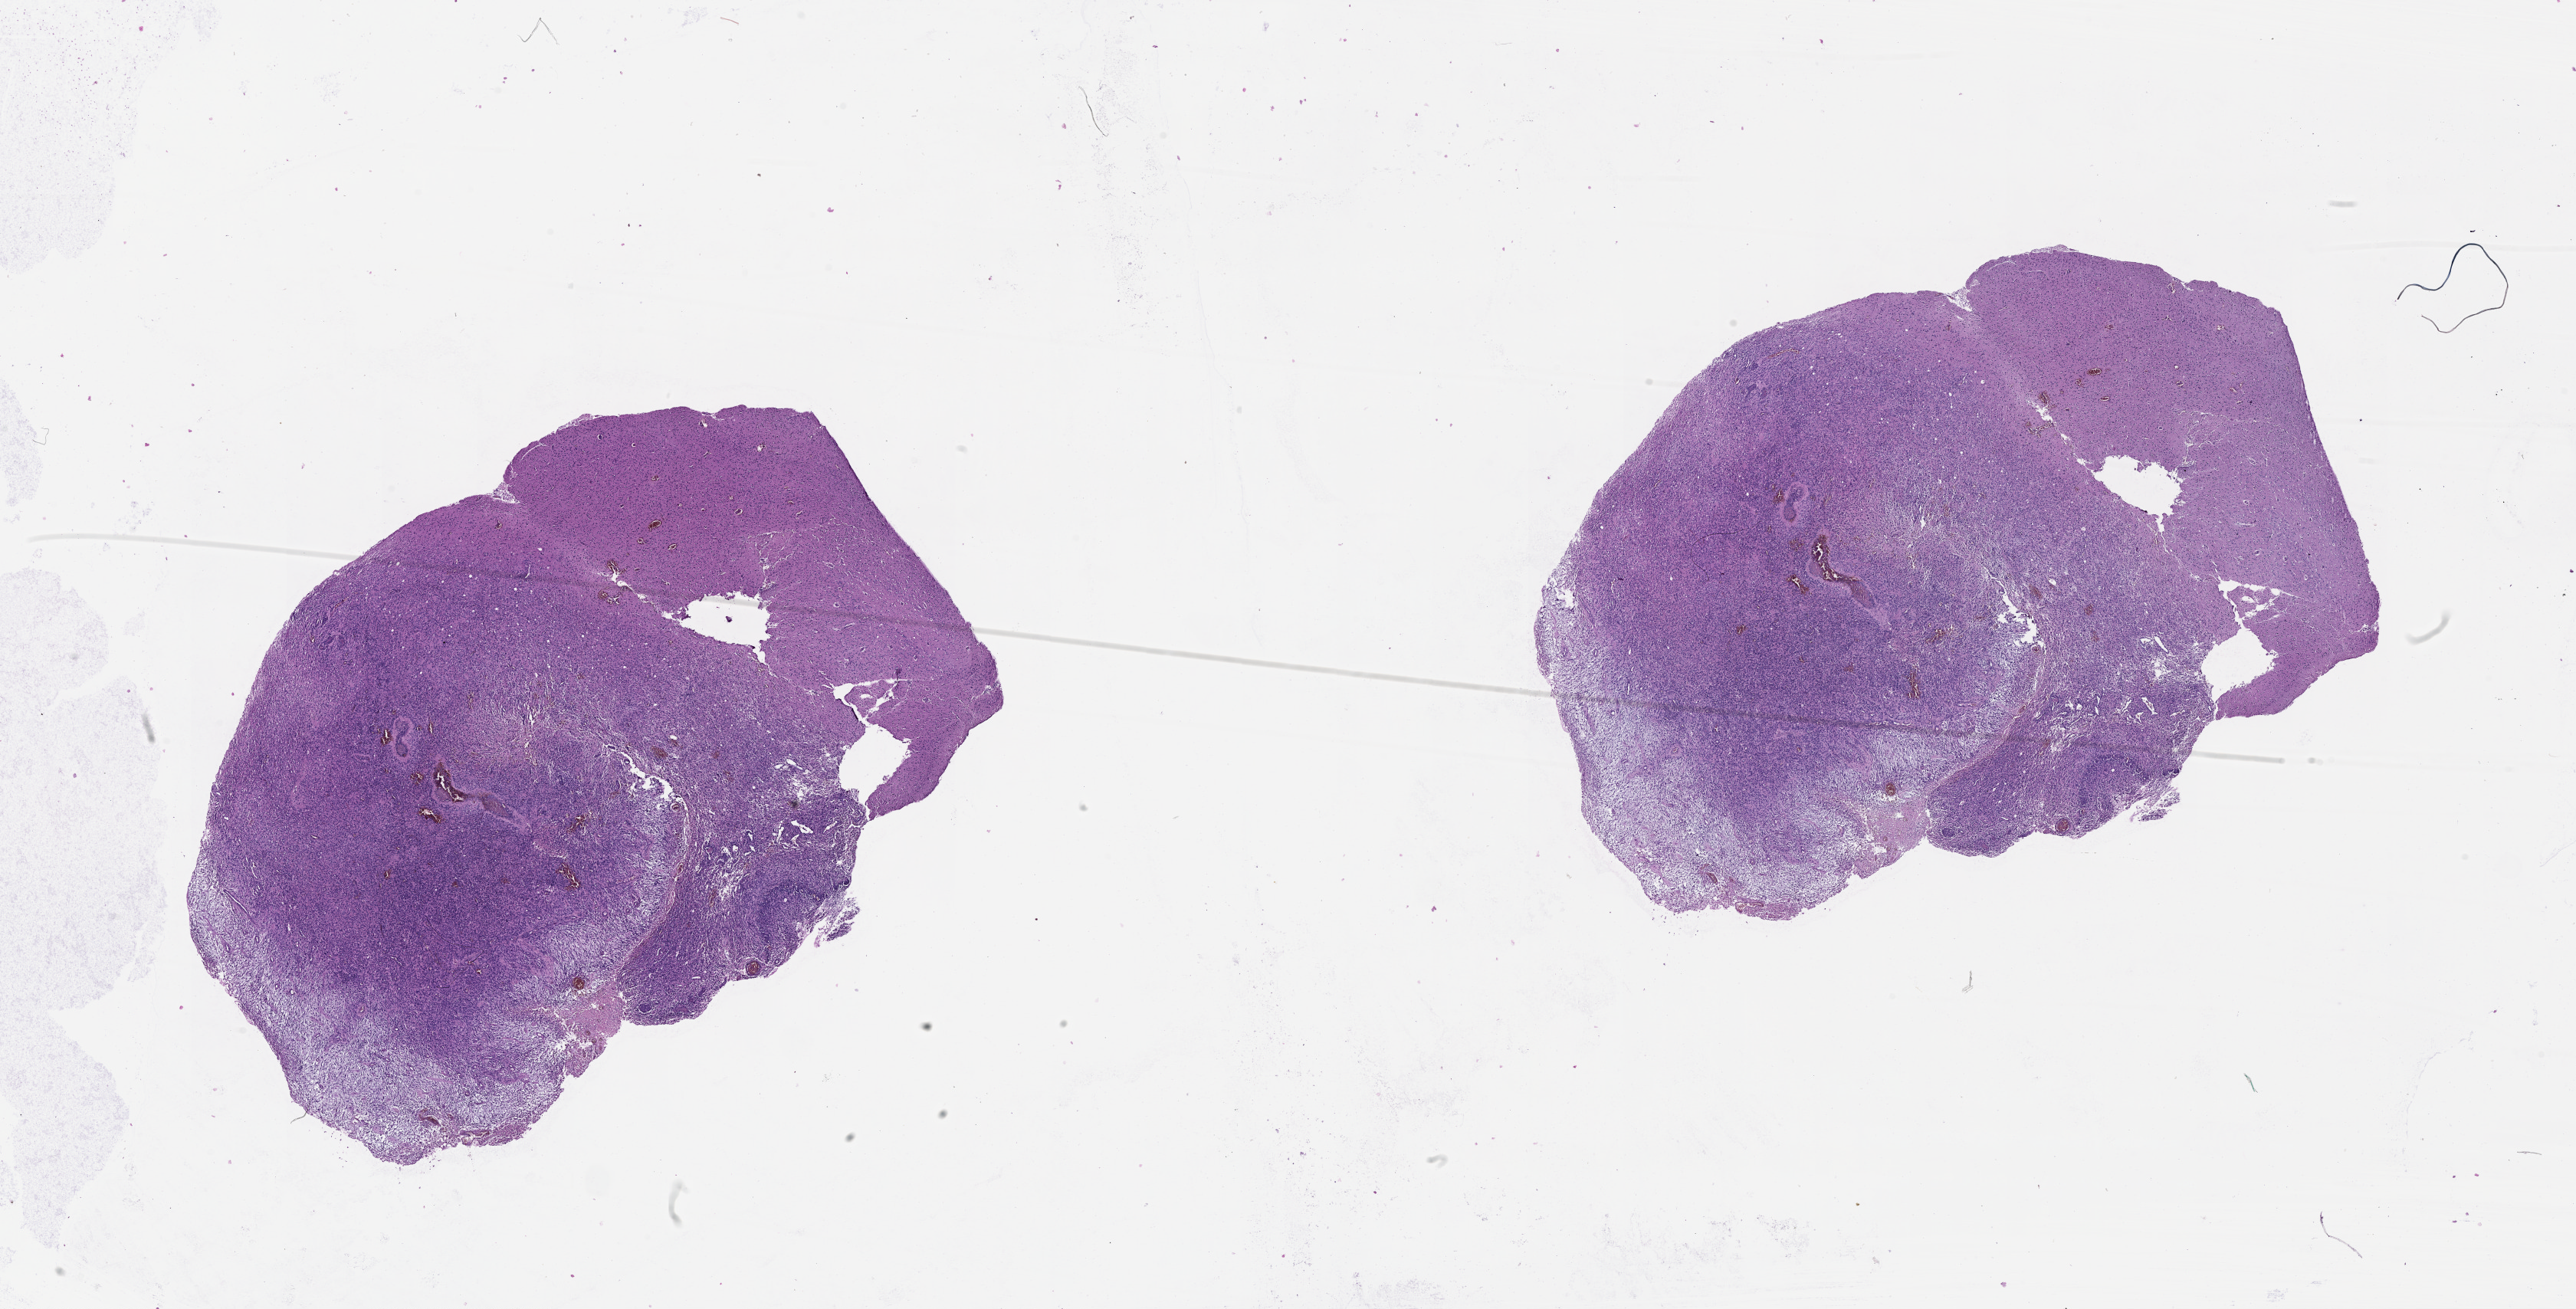
H&E-stained whole-slide image, low-resolution overview of the scanned area, about 27.1 x 13.8 mm; brain, tumour tissue. Male, 65 y/o.
Primary tumour site (as recorded): parietal lobe. Diagnosis: Glioblastoma.